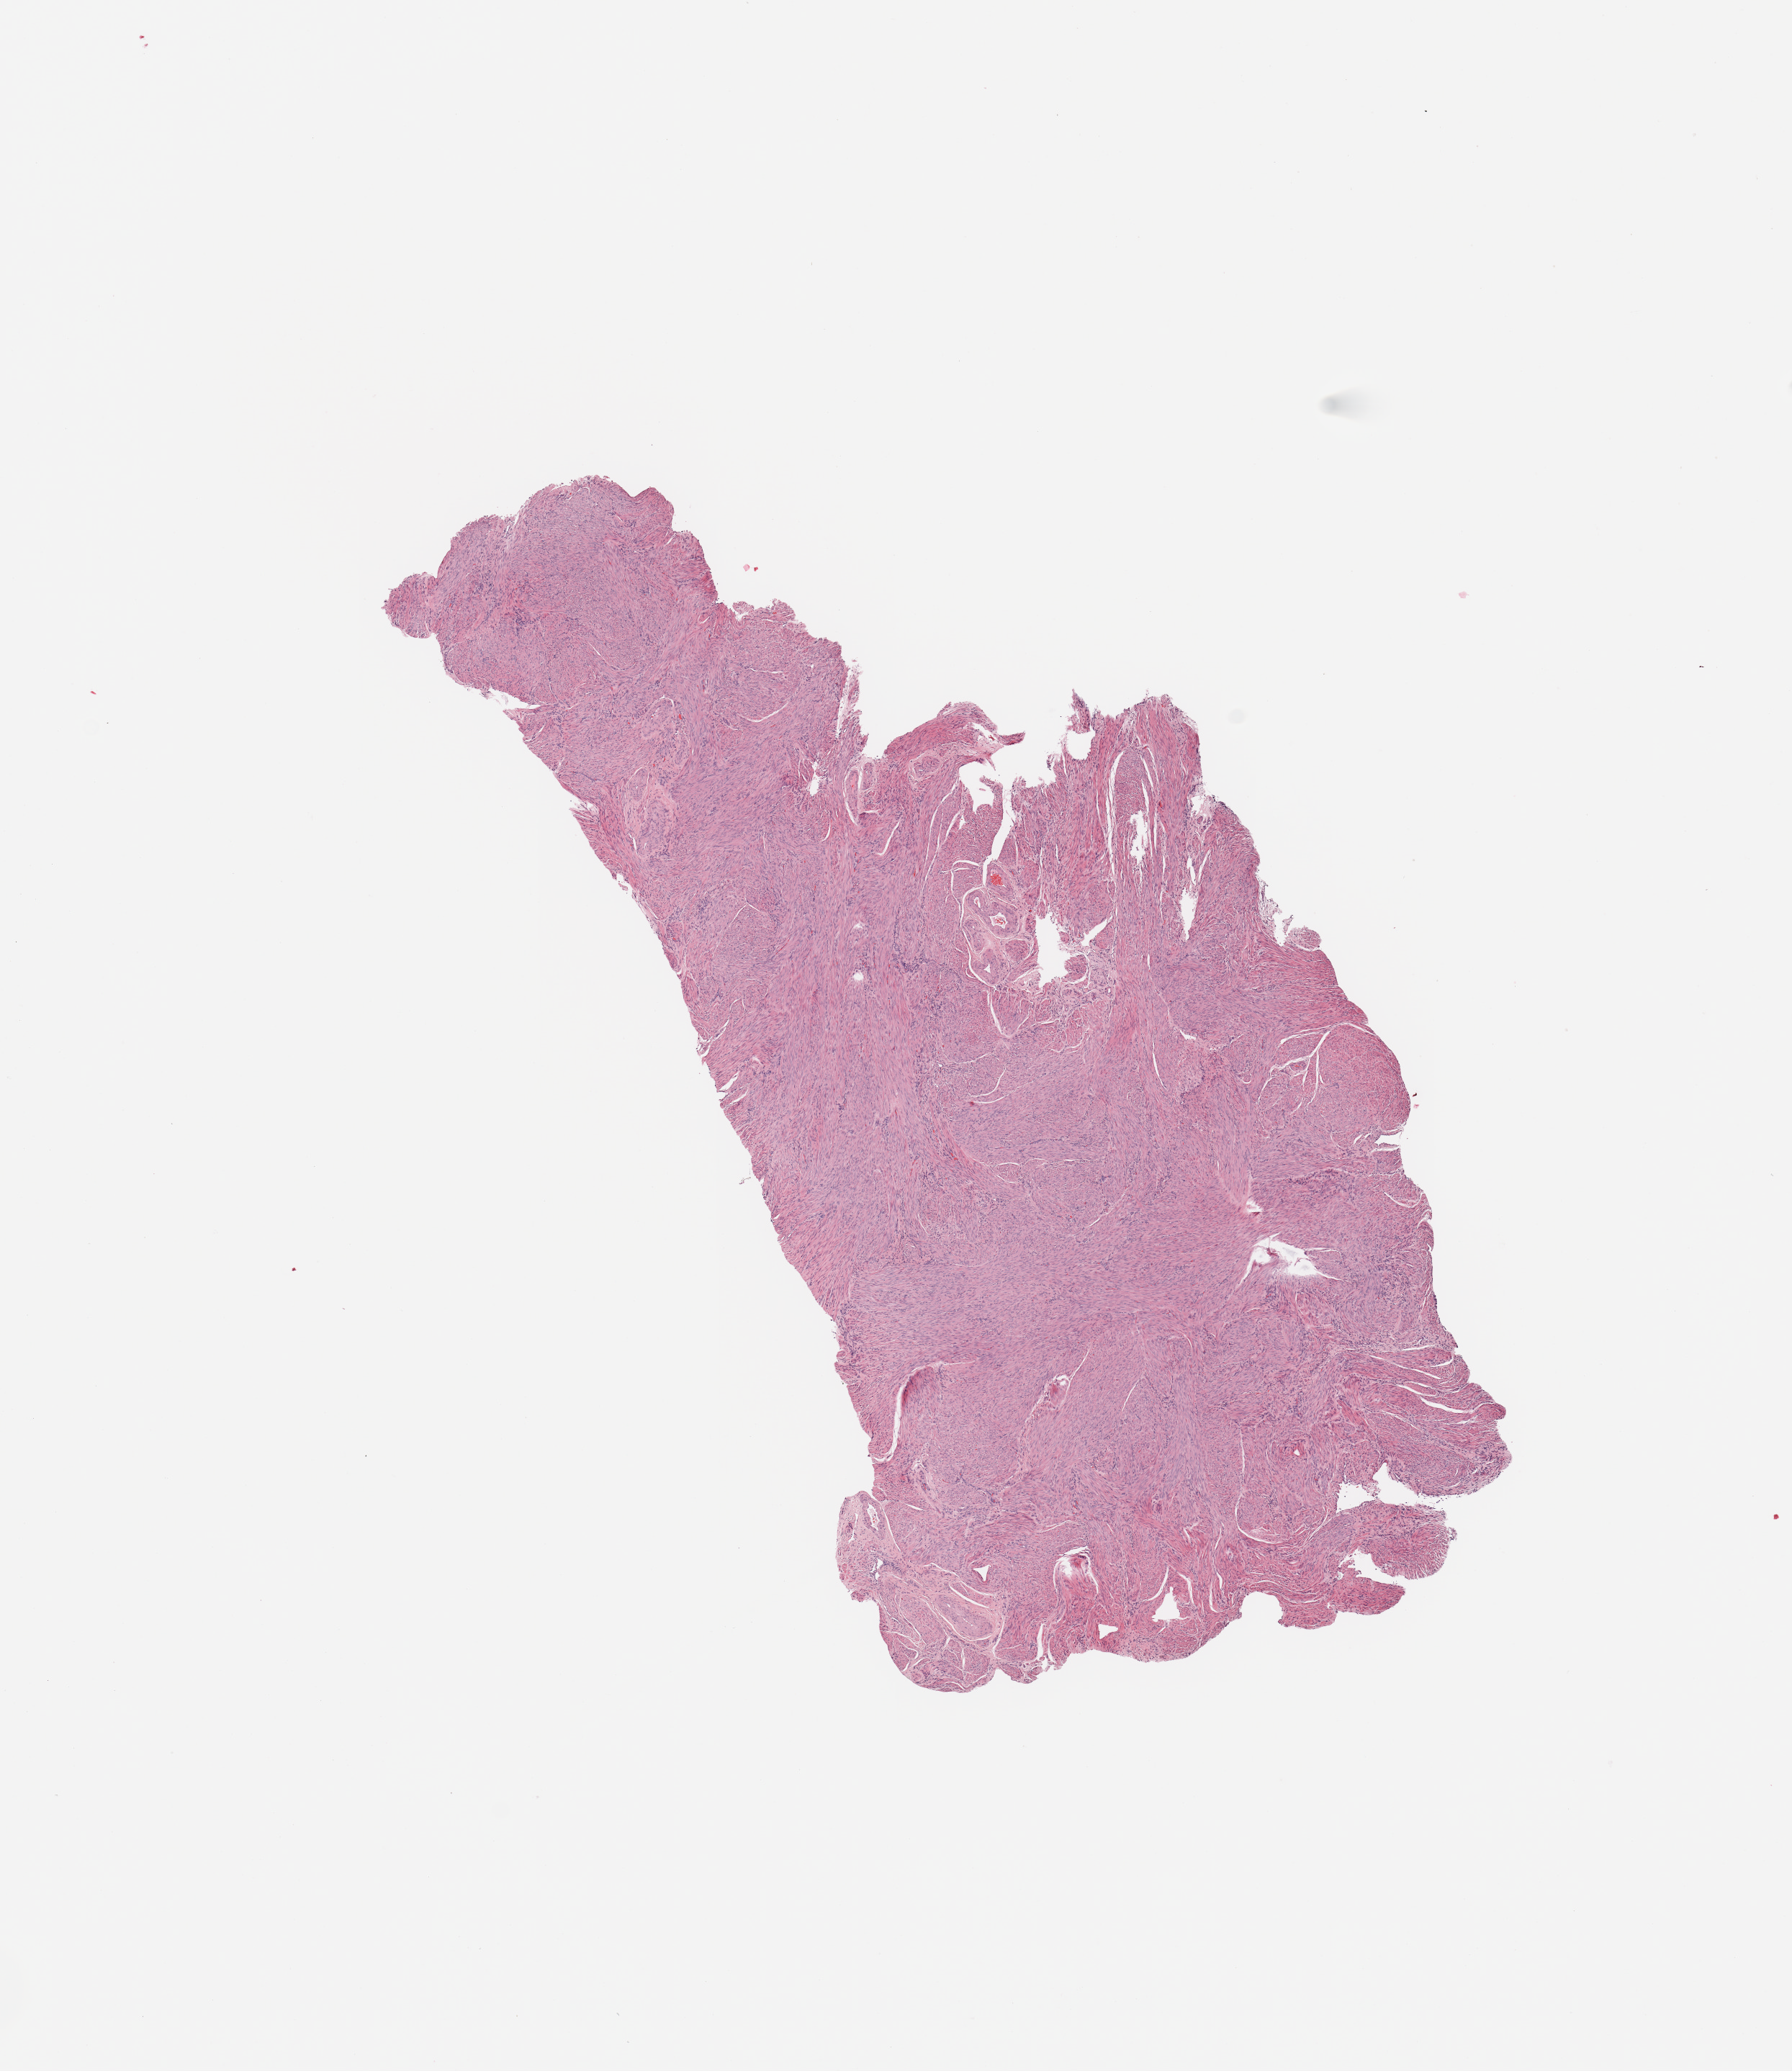
Hematoxylin and eosin (H&E) stained whole-slide image, shown as a low-resolution overview of the whole scanned area (about 9.8 x 11.4 mm). Uterus, normal (non-tumour) tissue. Patient: female, age 59 years.
This section: normal (non-tumour) tissue from the same patient. Patient diagnosis: Endometrioid adenocarcinoma, NOS.